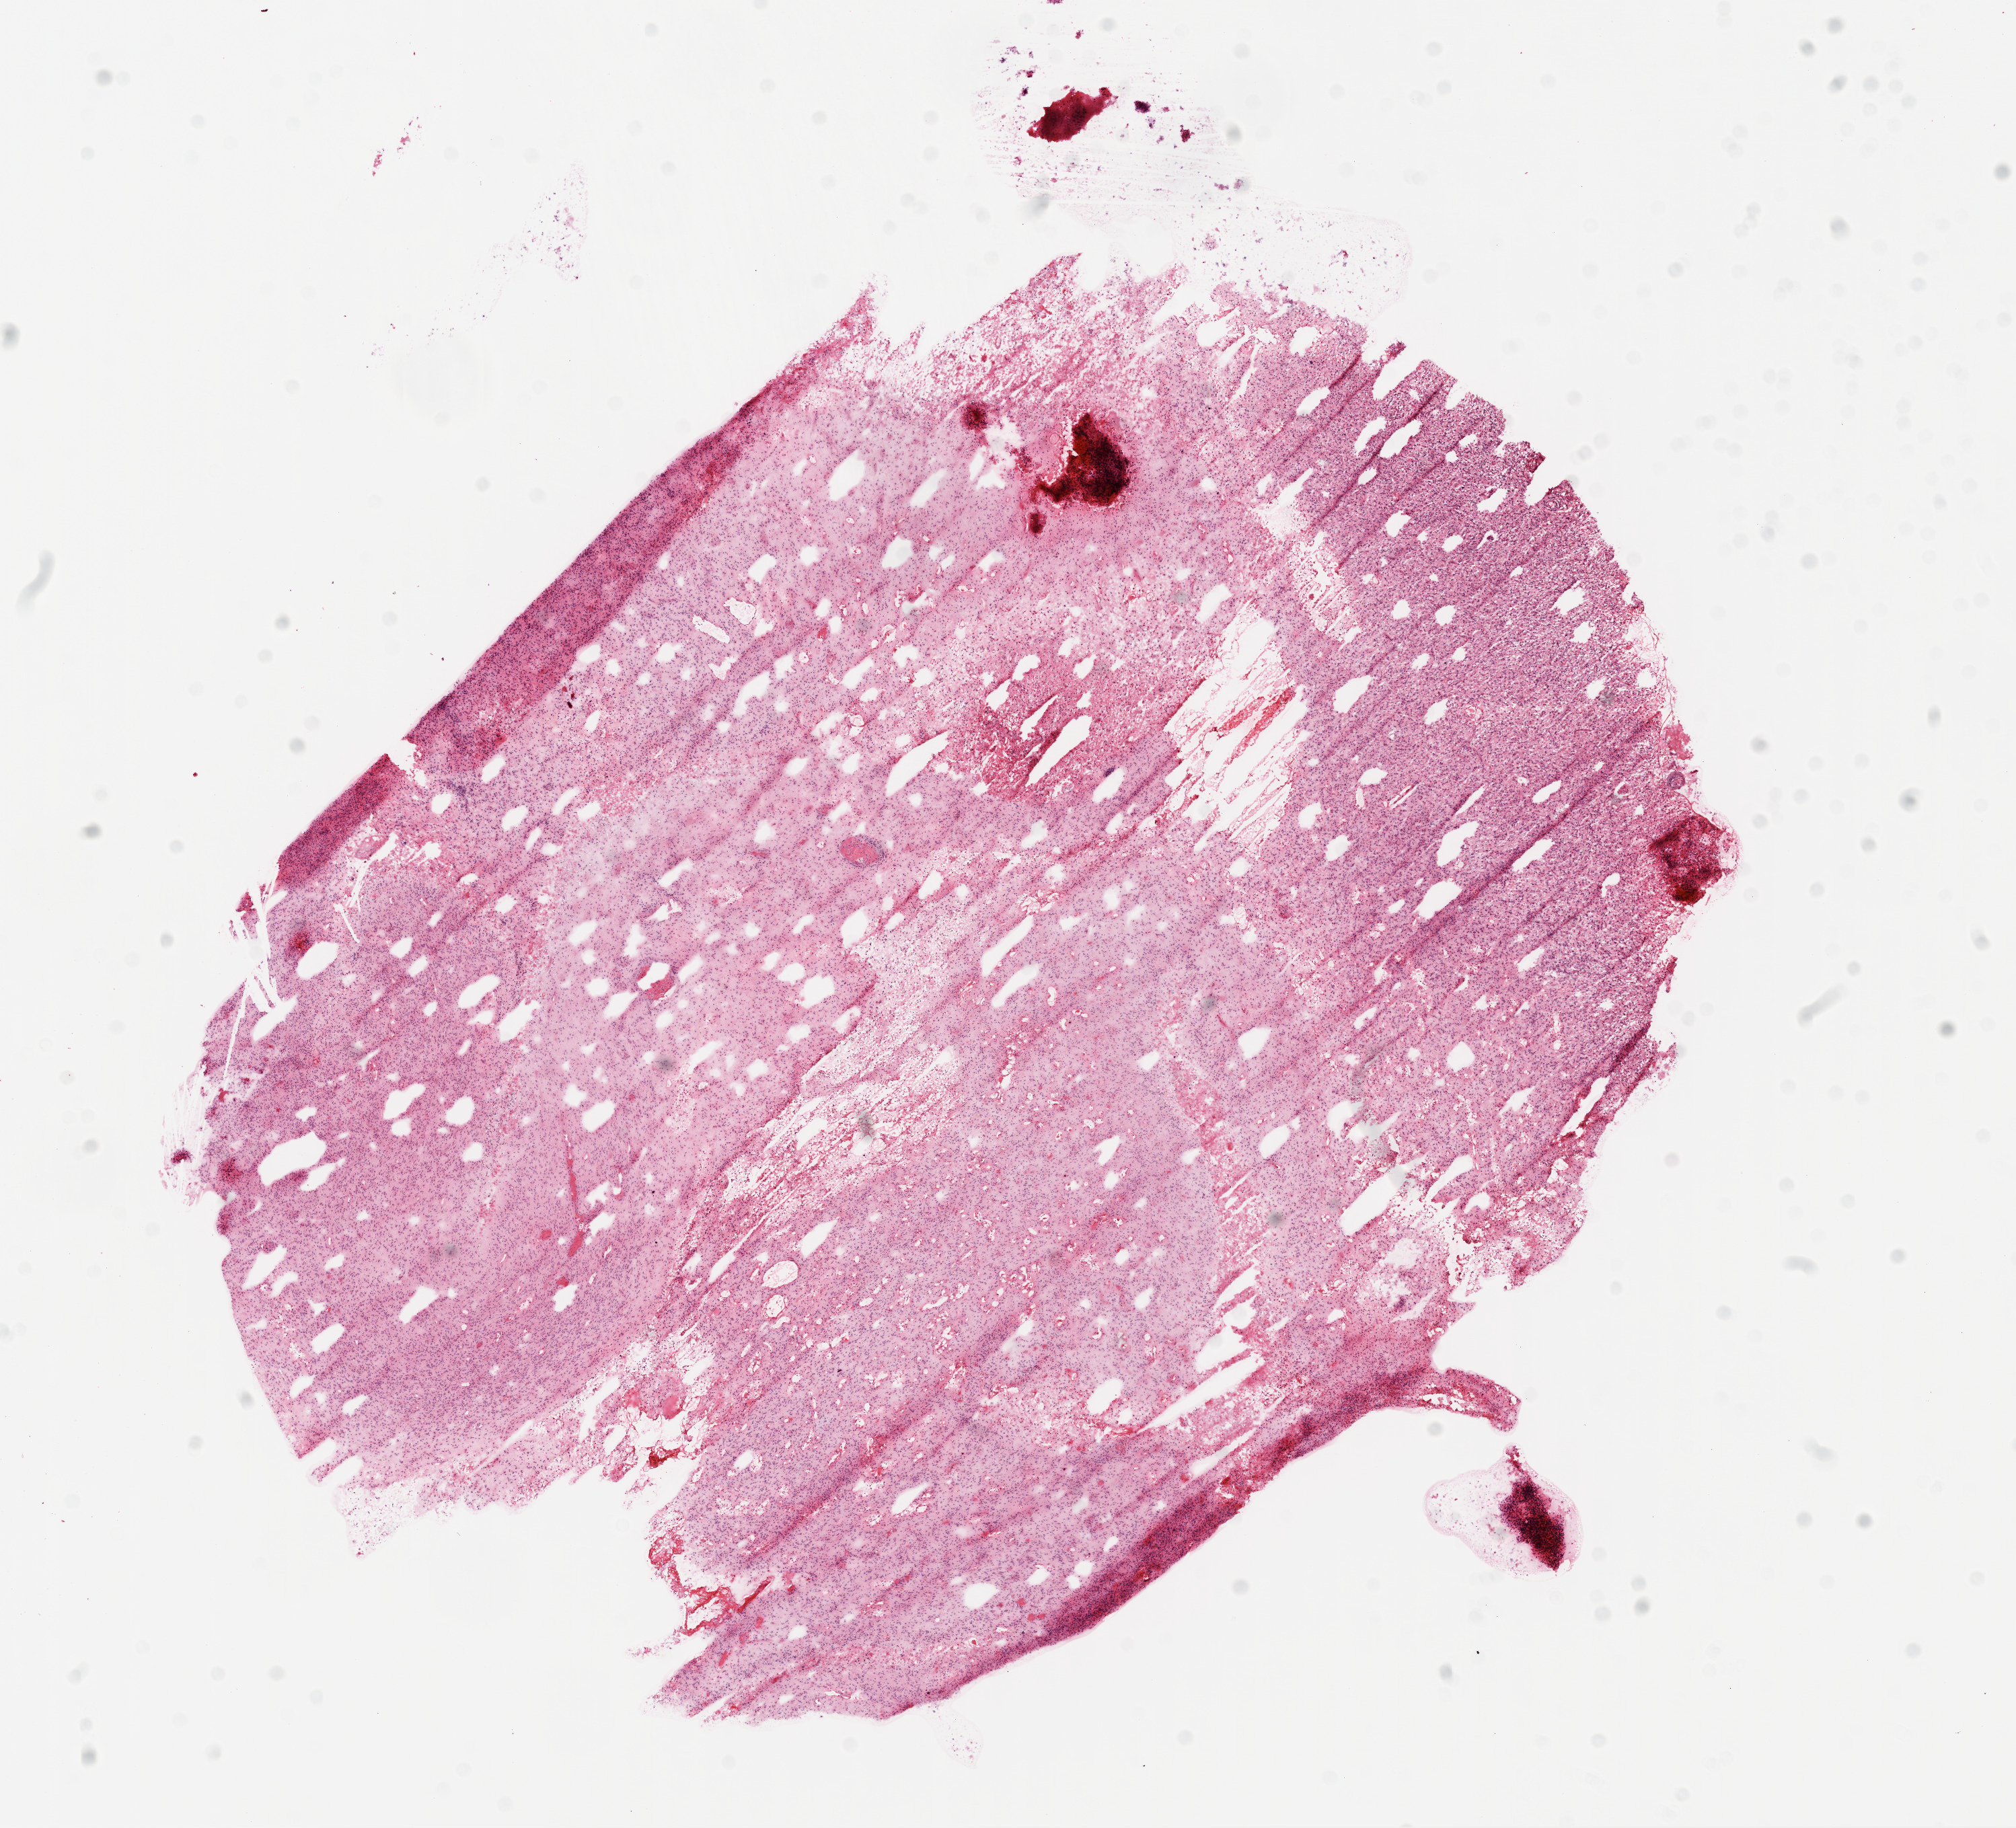
Whole-slide histology image, Hematoxylin and eosin (H&E) stained, shown as a low-resolution overview of the whole scanned area (about 12.1 x 11.0 mm, from a 20x scan). Frozen section from the bottom of the tissue portion. Primary tumour sample from the brain. Female patient; age at initial diagnosis 52 years. Pathologist review of this section (percent, as recorded): tumour cells 80%, tumour nuclei 90%, normal cells 0%, stromal cells 15%, necrosis 5%.
* pathologic diagnosis: Glioblastoma